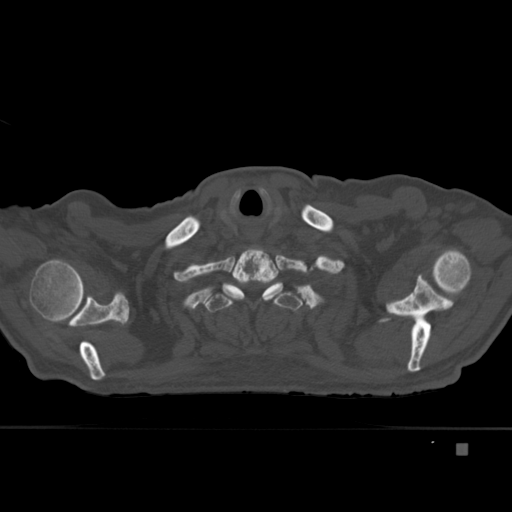
CT including the spine, one axial slice. Position 354 of 451 along the scan axis. Bone window (W 1800 / L 400 HU). 1.5 mm slice thickness. 512 × 512 image matrix, field of view 378 × 378 mm. Male patient, age 75 years. From the clinical record (not read from this slice): primary cancer: prostate.
Structures marked on this image (semi-automatically segmented with operator editing):
- T1 vertebra: bounding box (x1, y1, x2, y2) in pixels: (222, 248, 283, 303)
- T2 vertebra: (203, 284, 303, 312)